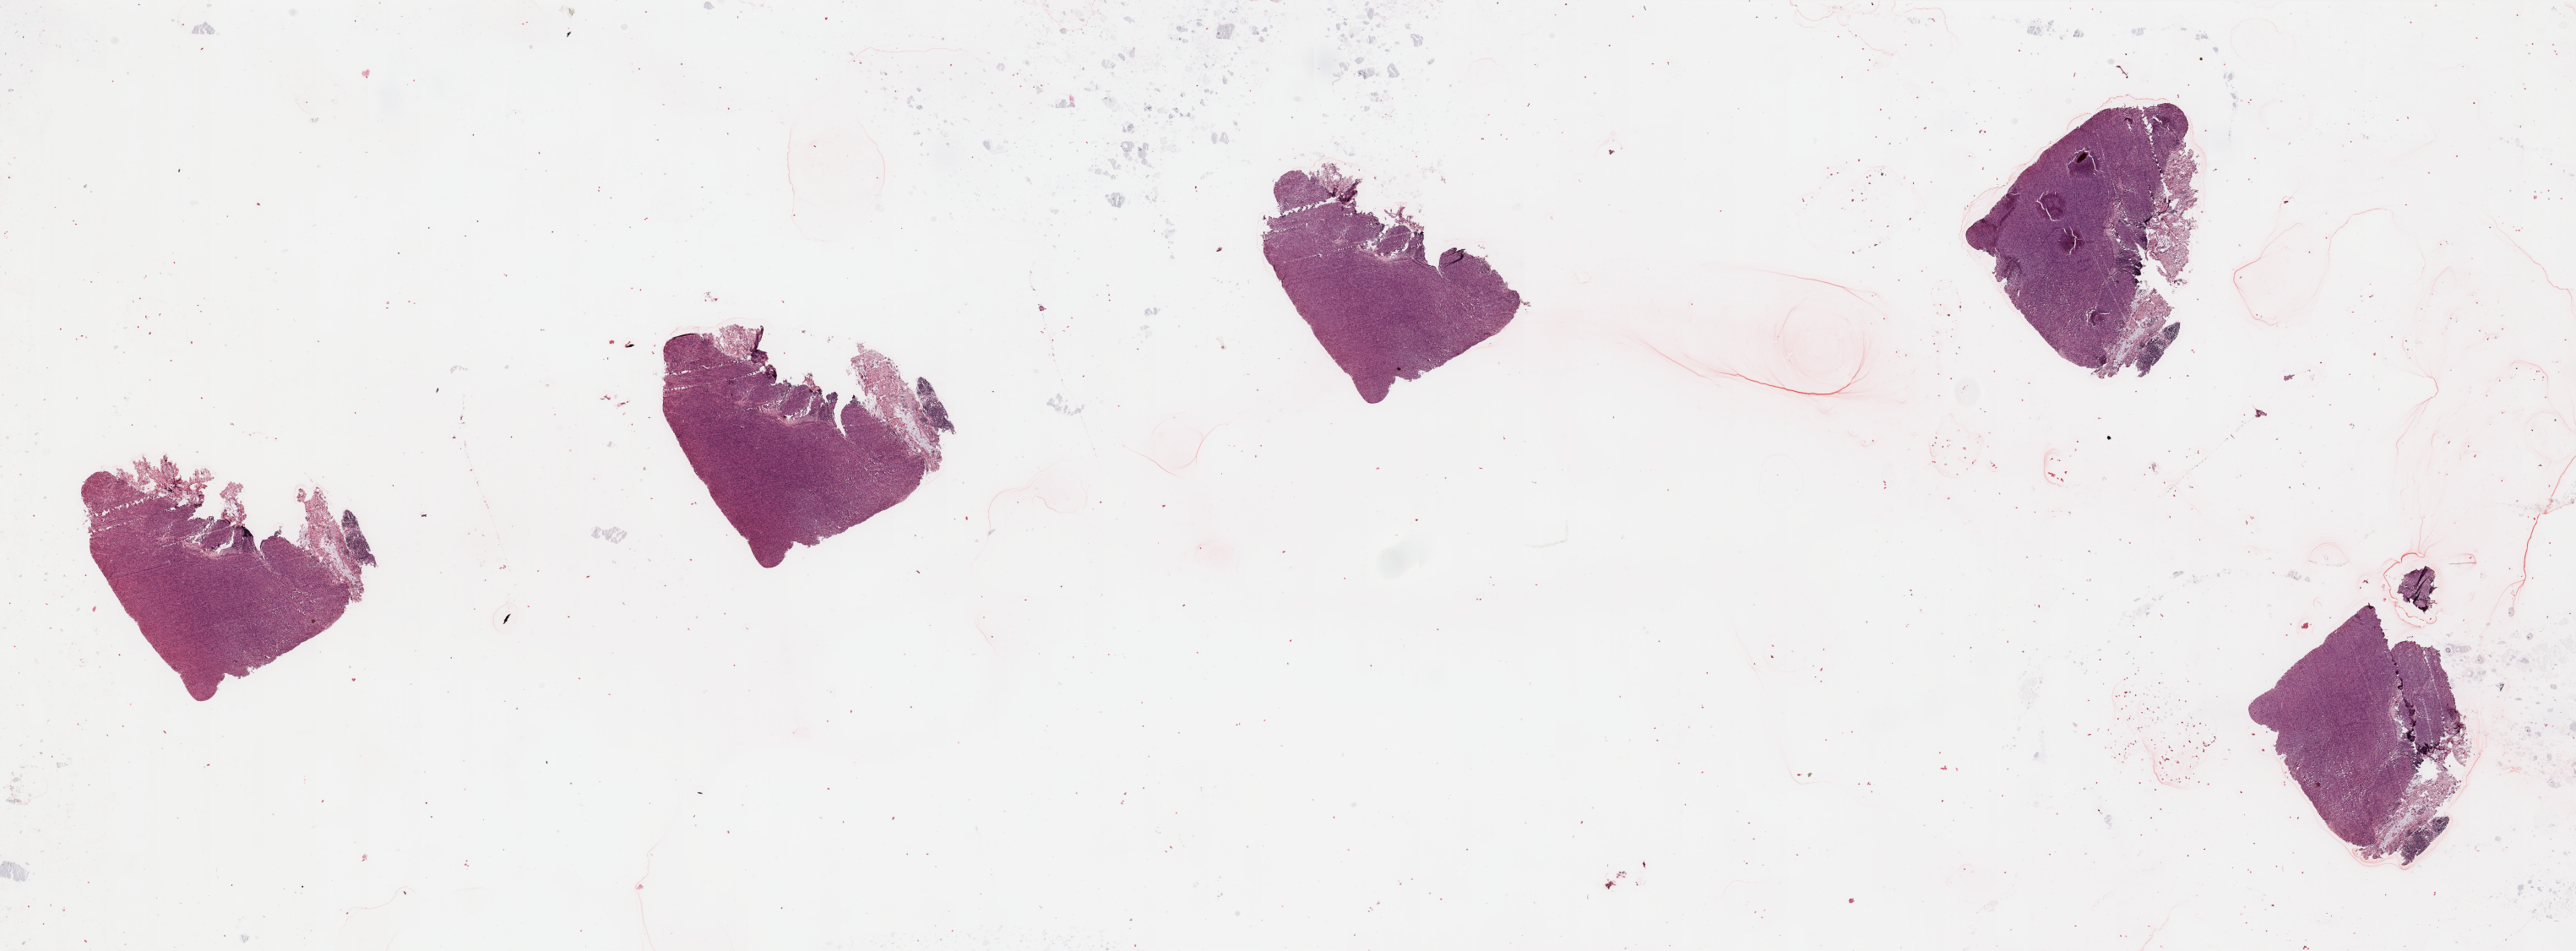
Digitized Hematoxylin and eosin (H&E) stained tissue section (whole slide) — low-resolution overview of the scanned area, about 48.2 x 17.8 mm (acquisition: 20x scan); tumour tissue sample, sampled site: lymph node. 84-year-old male patient. Composition of this section per pathologist review: tumour nuclei 90%, necrosis 0%.
This section: metastatic tumour tissue. Patient diagnosis: Malignant melanoma, NOS.